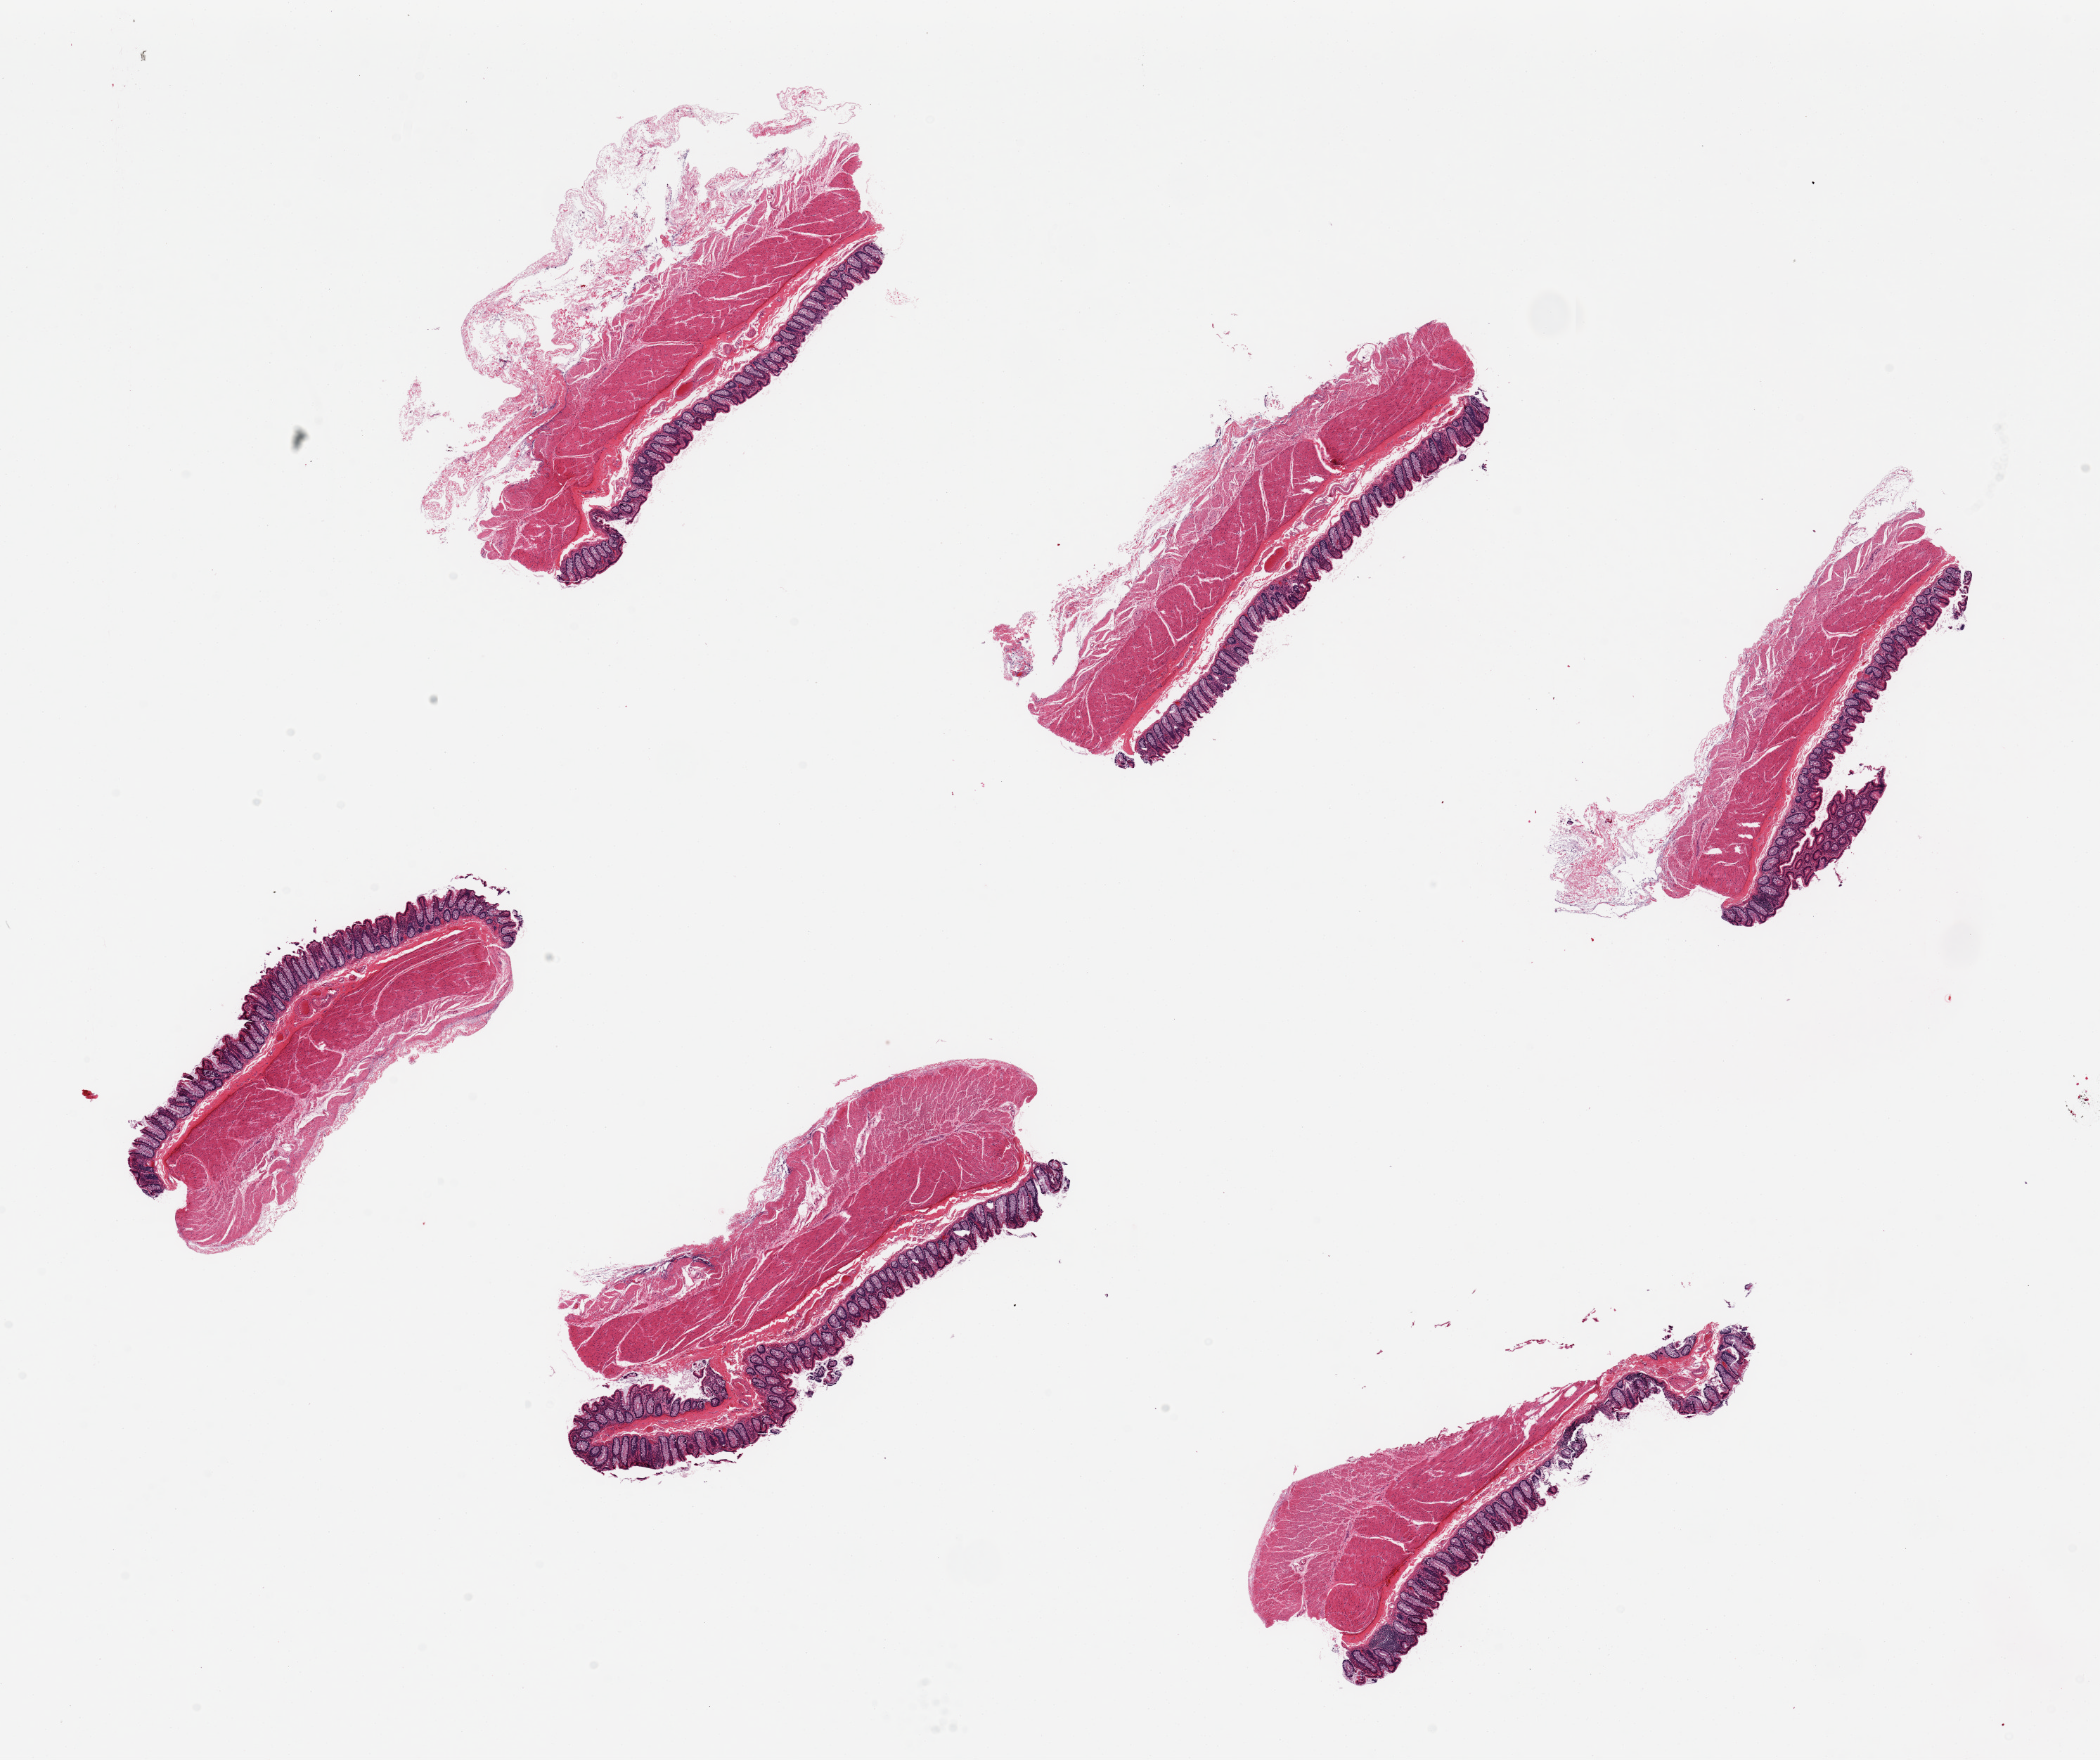
H&E whole-slide image — low-resolution overview of the scanned area, about 23.6 x 19.8 mm (acquisition: 20x scan), PAXgene-fixed paraffin-embedded (PFPE) section, target tissue: transverse colon, tissue donor sample. Donor sex: female.
- reviewer comment on this tissue sample: 6 pieces, ~6x2mm; mucosa moderately well-preserved, ~10-15% of thickness